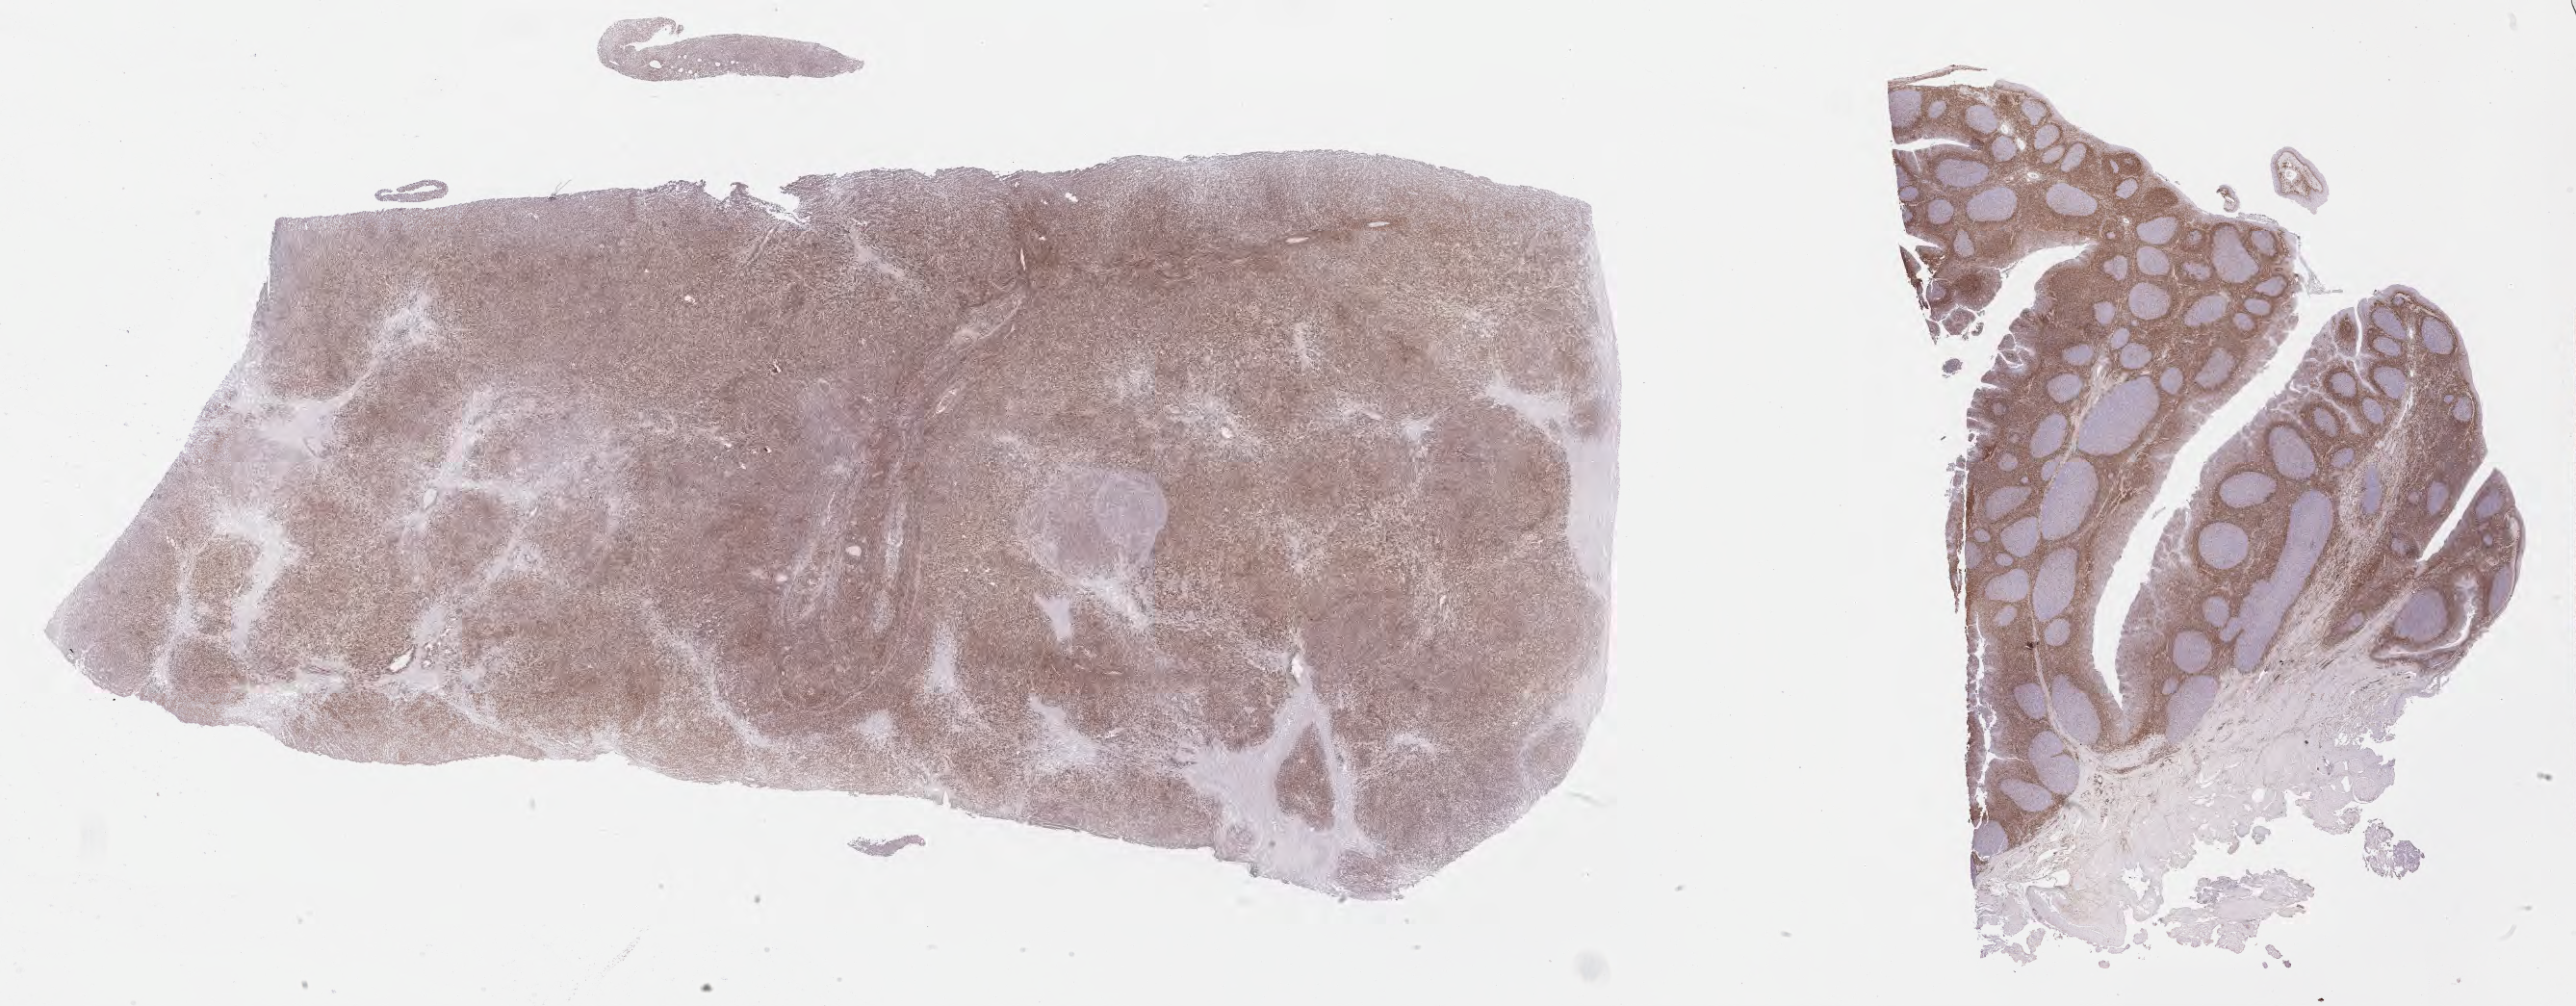
Immunohistochemistry (IHC) whole-slide image stained for BCL2, a low-resolution overview of the entire scanned area, about 43.3 x 16.9 mm, tumor tissue. Patient: male, aged 39.
- diagnosis: Diffuse large B-cell lymphoma, NOS